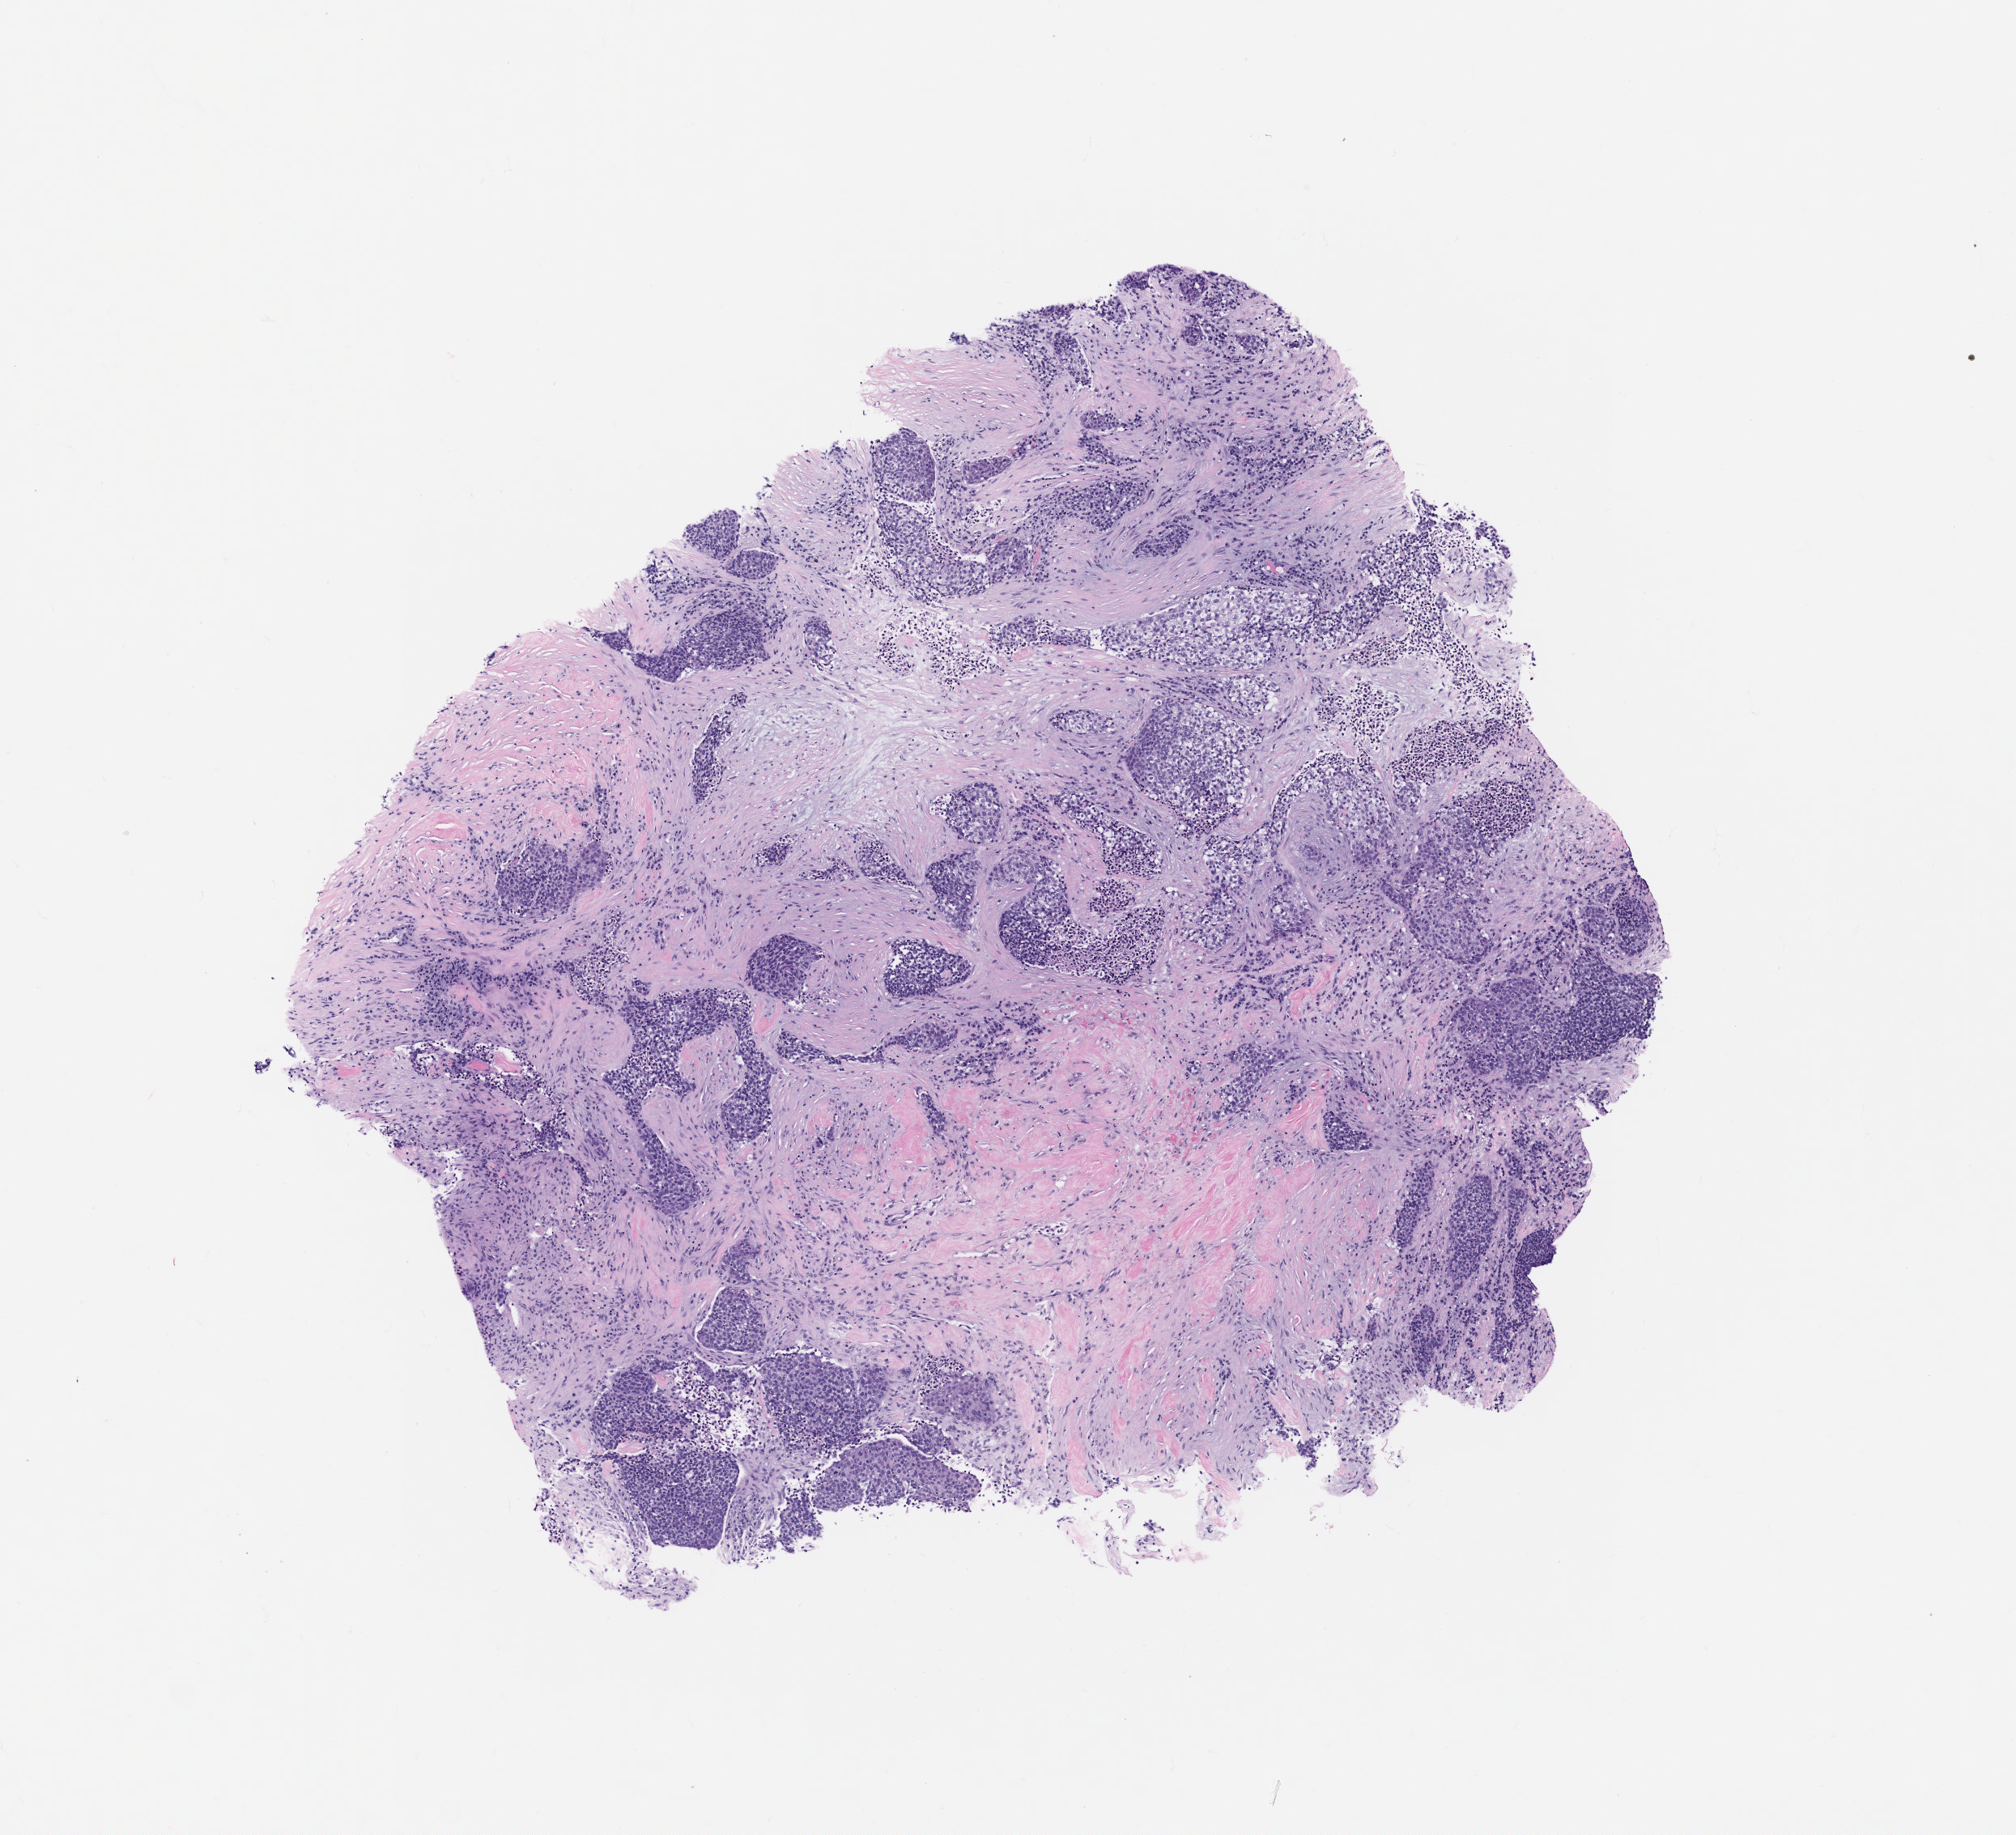
Haematoxylin and eosin whole-slide image of the patient's (originator) tumor tissue, a low-resolution overview of the entire scanned area, about 5.0 x 4.6 mm; formalin-fixed, paraffin-embedded (FFPE) tissue; originating tumor site category: head and neck. Male patient, 69 years old.
Diagnosis: Head and Neck Squamous Cell Carcinoma.